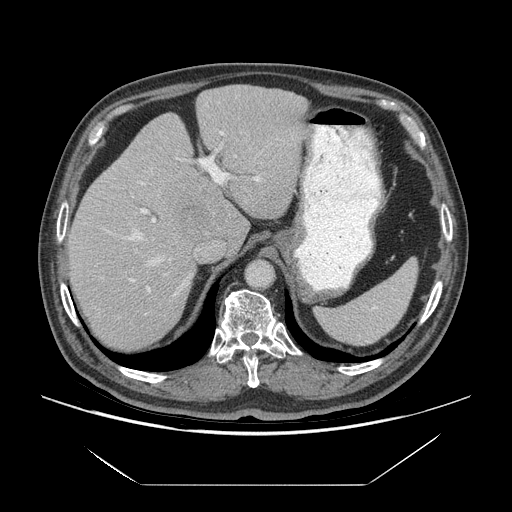
Contrast-enhanced abdominal CT (liver protocol), one axial slice; slice 49 of 75 in the series (ordered by position); reconstruction kernel STANDARD; 140 kVp; soft-tissue window (W 400 / L 40 HU); 512 × 512 image matrix. From the clinical record (not read from this slice): diagnosis: hepatocellular carcinoma (patient treated with transarterial chemoembolisation; whether this scan precedes or follows treatment is not stated here); TNM stage (as recorded): Stage-I.
Structures marked on this image (semi-automatic segmentation, software-assisted and operator-edited):
- liver parenchyma outside the tumour (the mass and vessels are separate outlines, so this box may not span the whole liver): bounding box (x1, y1, x2, y2) in pixels: (67, 84, 308, 348)
- mass: (172, 169, 226, 242)
- liver vessels: (104, 131, 261, 296)